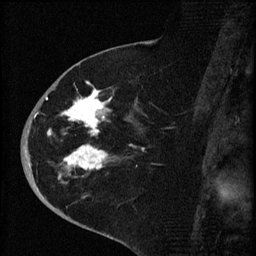
Breast MRI (dynamic contrast-enhanced), one sagittal slice; slice 31 of 60 in the series (ordered by position); dynamic contrast-enhanced series, image 2 of 4 at this slice position (ordered by acquisition); 1.5 T; TE 4.2 ms, TR 8.2 ms; 2 mm slice thickness; 256 × 256 image matrix, field of view 180 × 180 mm. Female patient, age 71 years.
Annotated regions visible in this slice (semi-automatic segmentation, software-assisted and operator-edited):
- analysis volume of interest (the breast-tissue region the enhancement analysis was run in; not a lesion): box from (x=35, y=75) to (x=148, y=190) px
- tumour enhancement mask (voxels above the 70 % enhancement threshold inside the analysis volume of interest): (x=35, y=81)–(x=112, y=179)